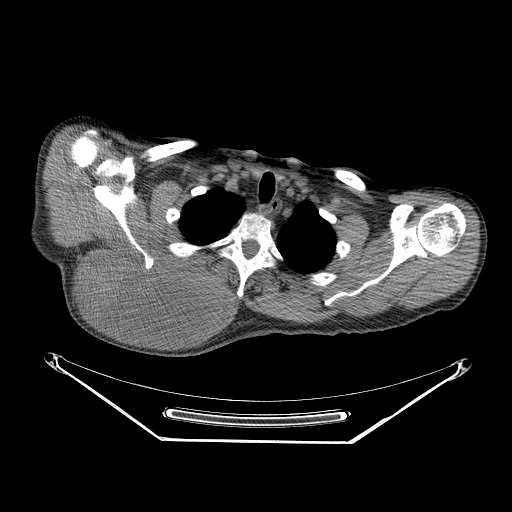
CT of an extremity soft-tissue mass (from a PET/CT study), one axial slice. Position 202 of 267 along the scan axis. Soft-tissue window (W 400 / L 40 HU). 3.75 mm slice thickness. 512 × 512 image matrix, field of view 500 × 500 mm. Male patient. From the clinical record (not read from this slice): histological type: pleiomorphic spindle cell undifferentiated; grade: high; site of the primary tumour: right parascapusular.
Structures marked on this image (expert contour drawn on MRI and transferred to this co-registered scan by the dataset authors):
- gross tumour volume including surrounding oedema: bounding box <80,246,234,332> (left, top, right, bottom; pixels)
- gross tumour volume (mass): <80,251,220,332>